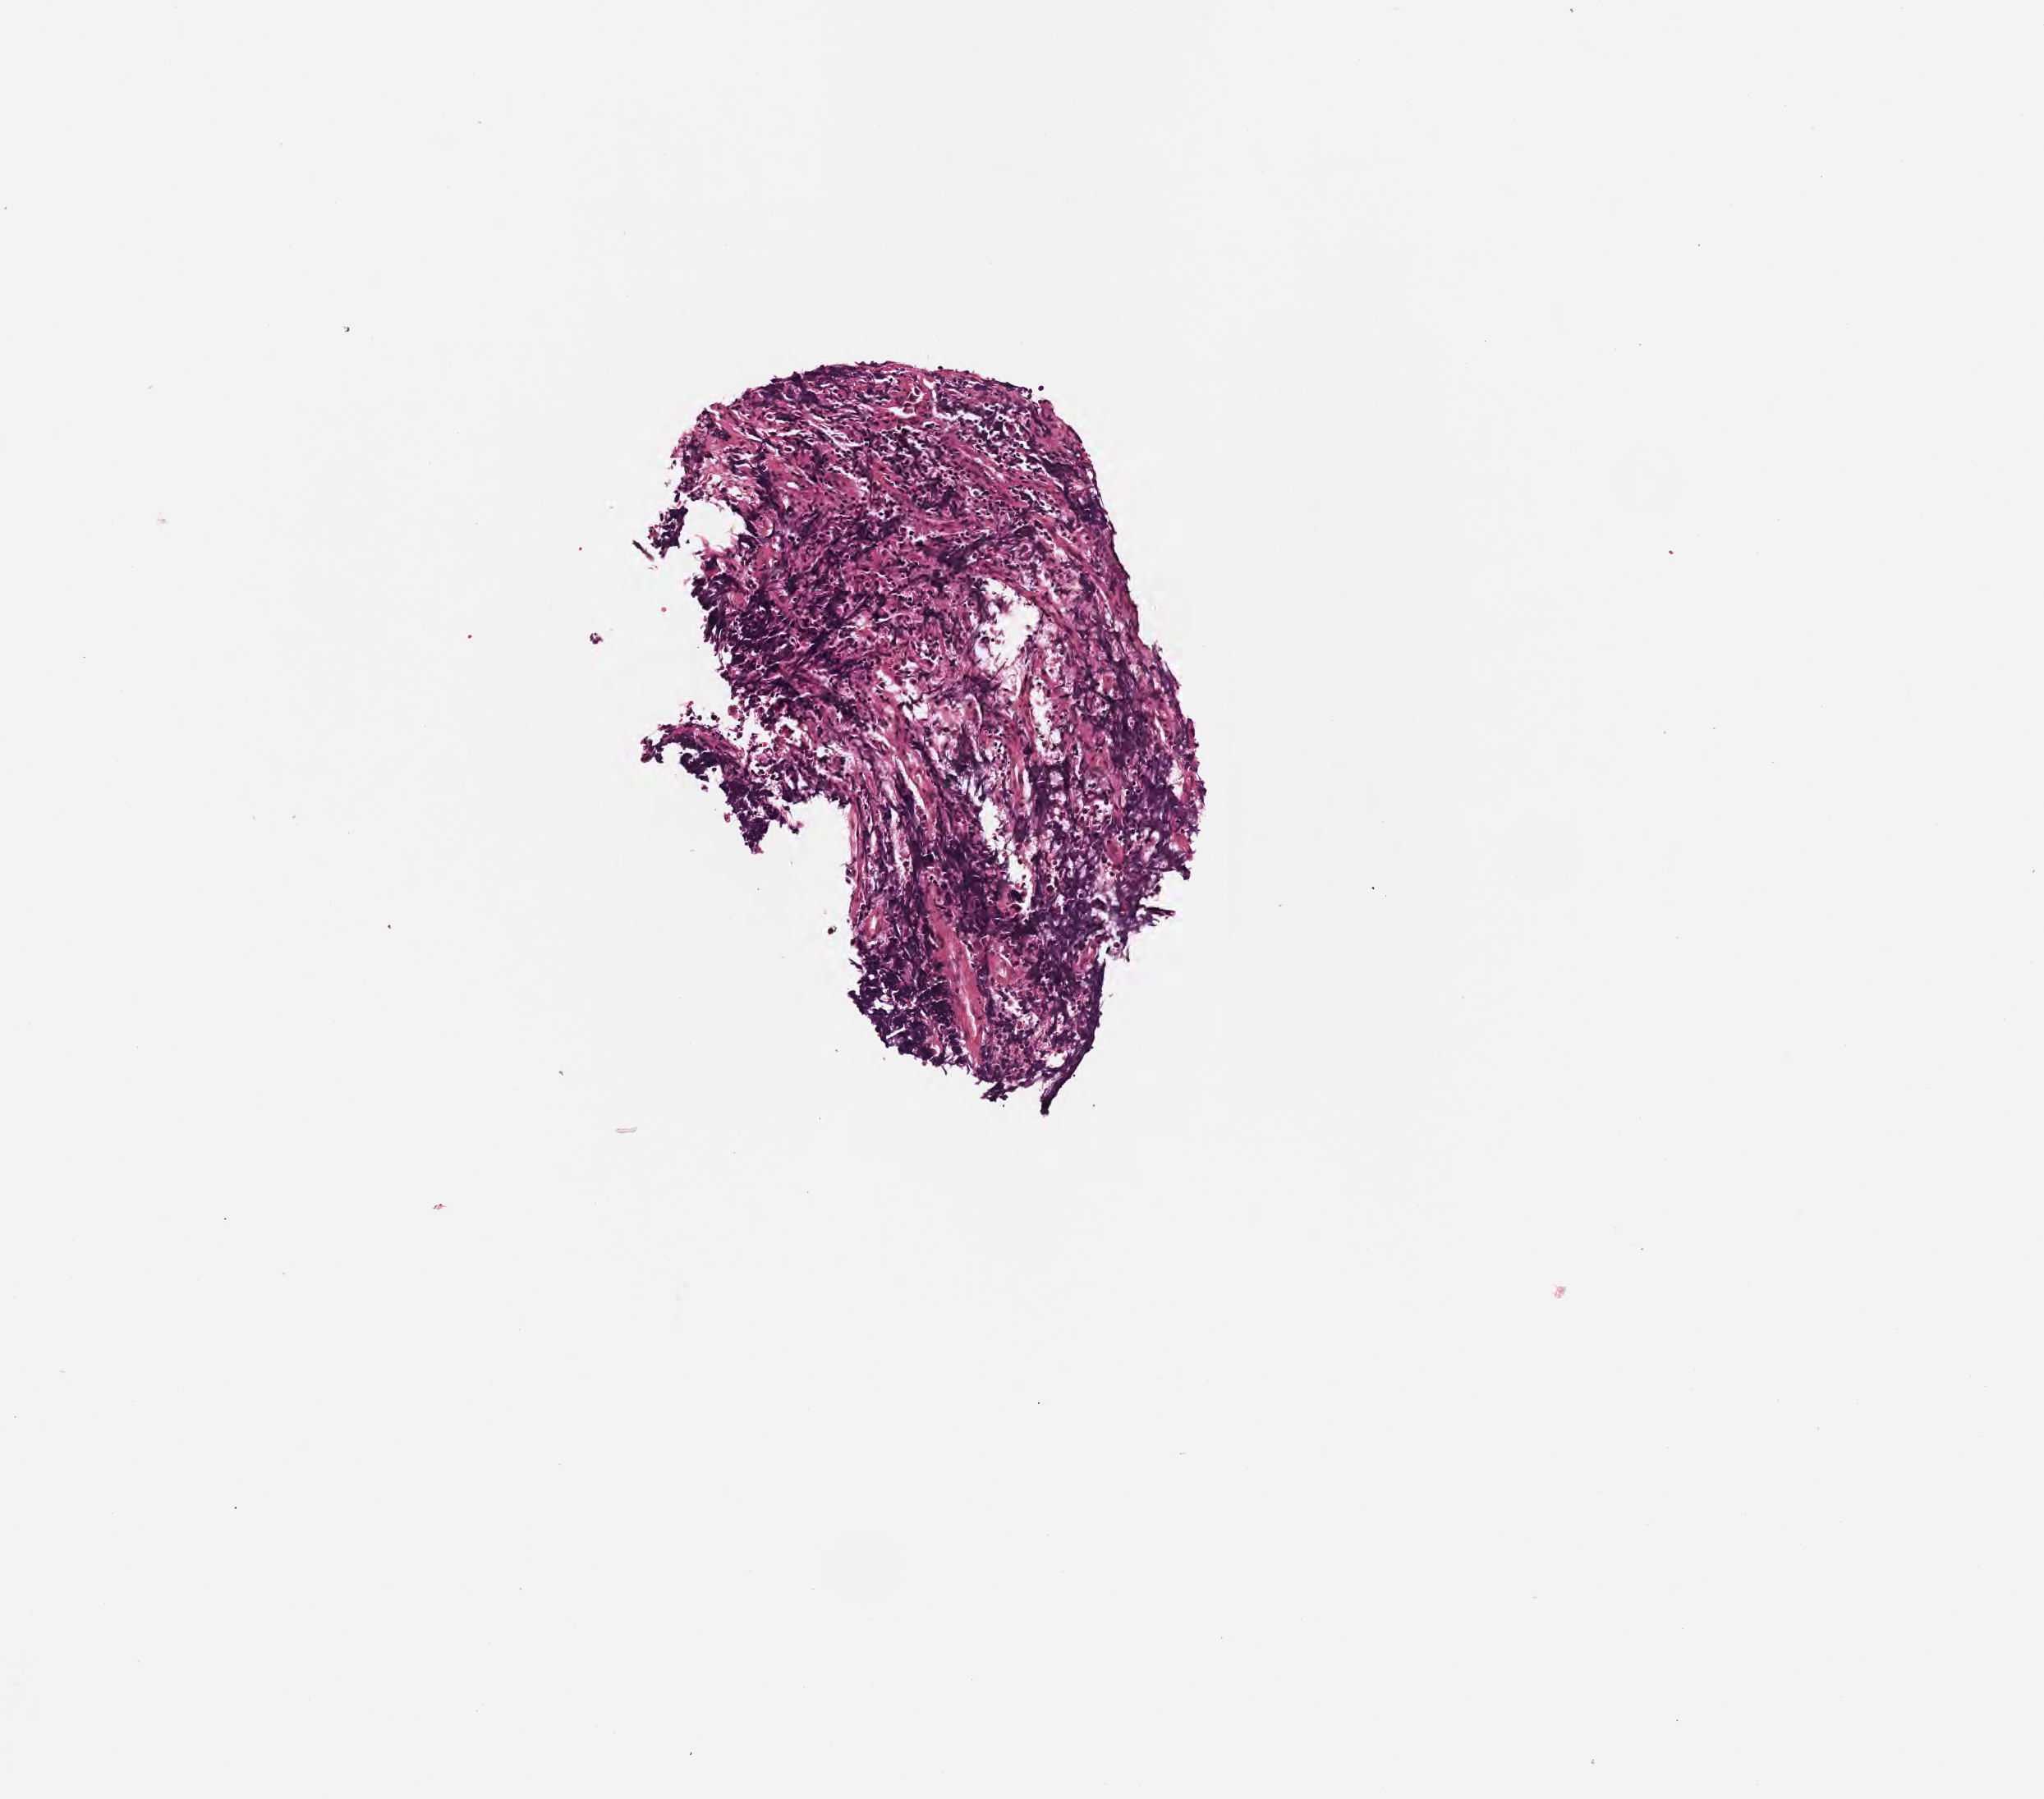
H&E whole-slide image — low-resolution overview of the scanned area, about 2.5 x 2.2 mm. Formalin-fixed, paraffin-embedded (FFPE) tissue. Specimen: primary tumor. Patient male; aged 10. Pathologist review of this section (percent, as recorded): tumor cells 60%, tumor nuclei 50%, stromal cells 20%, necrosis 20%, normal cells 0%. Inflammatory infiltration, as recorded: lymphocyte infiltration 70%, monocyte infiltration 20%, neutrophil infiltration 0%.
- section: bottom of the tissue portion
- Ann Arbor stage (patient): Stage IV
- diagnosis: Burkitt lymphoma, NOS